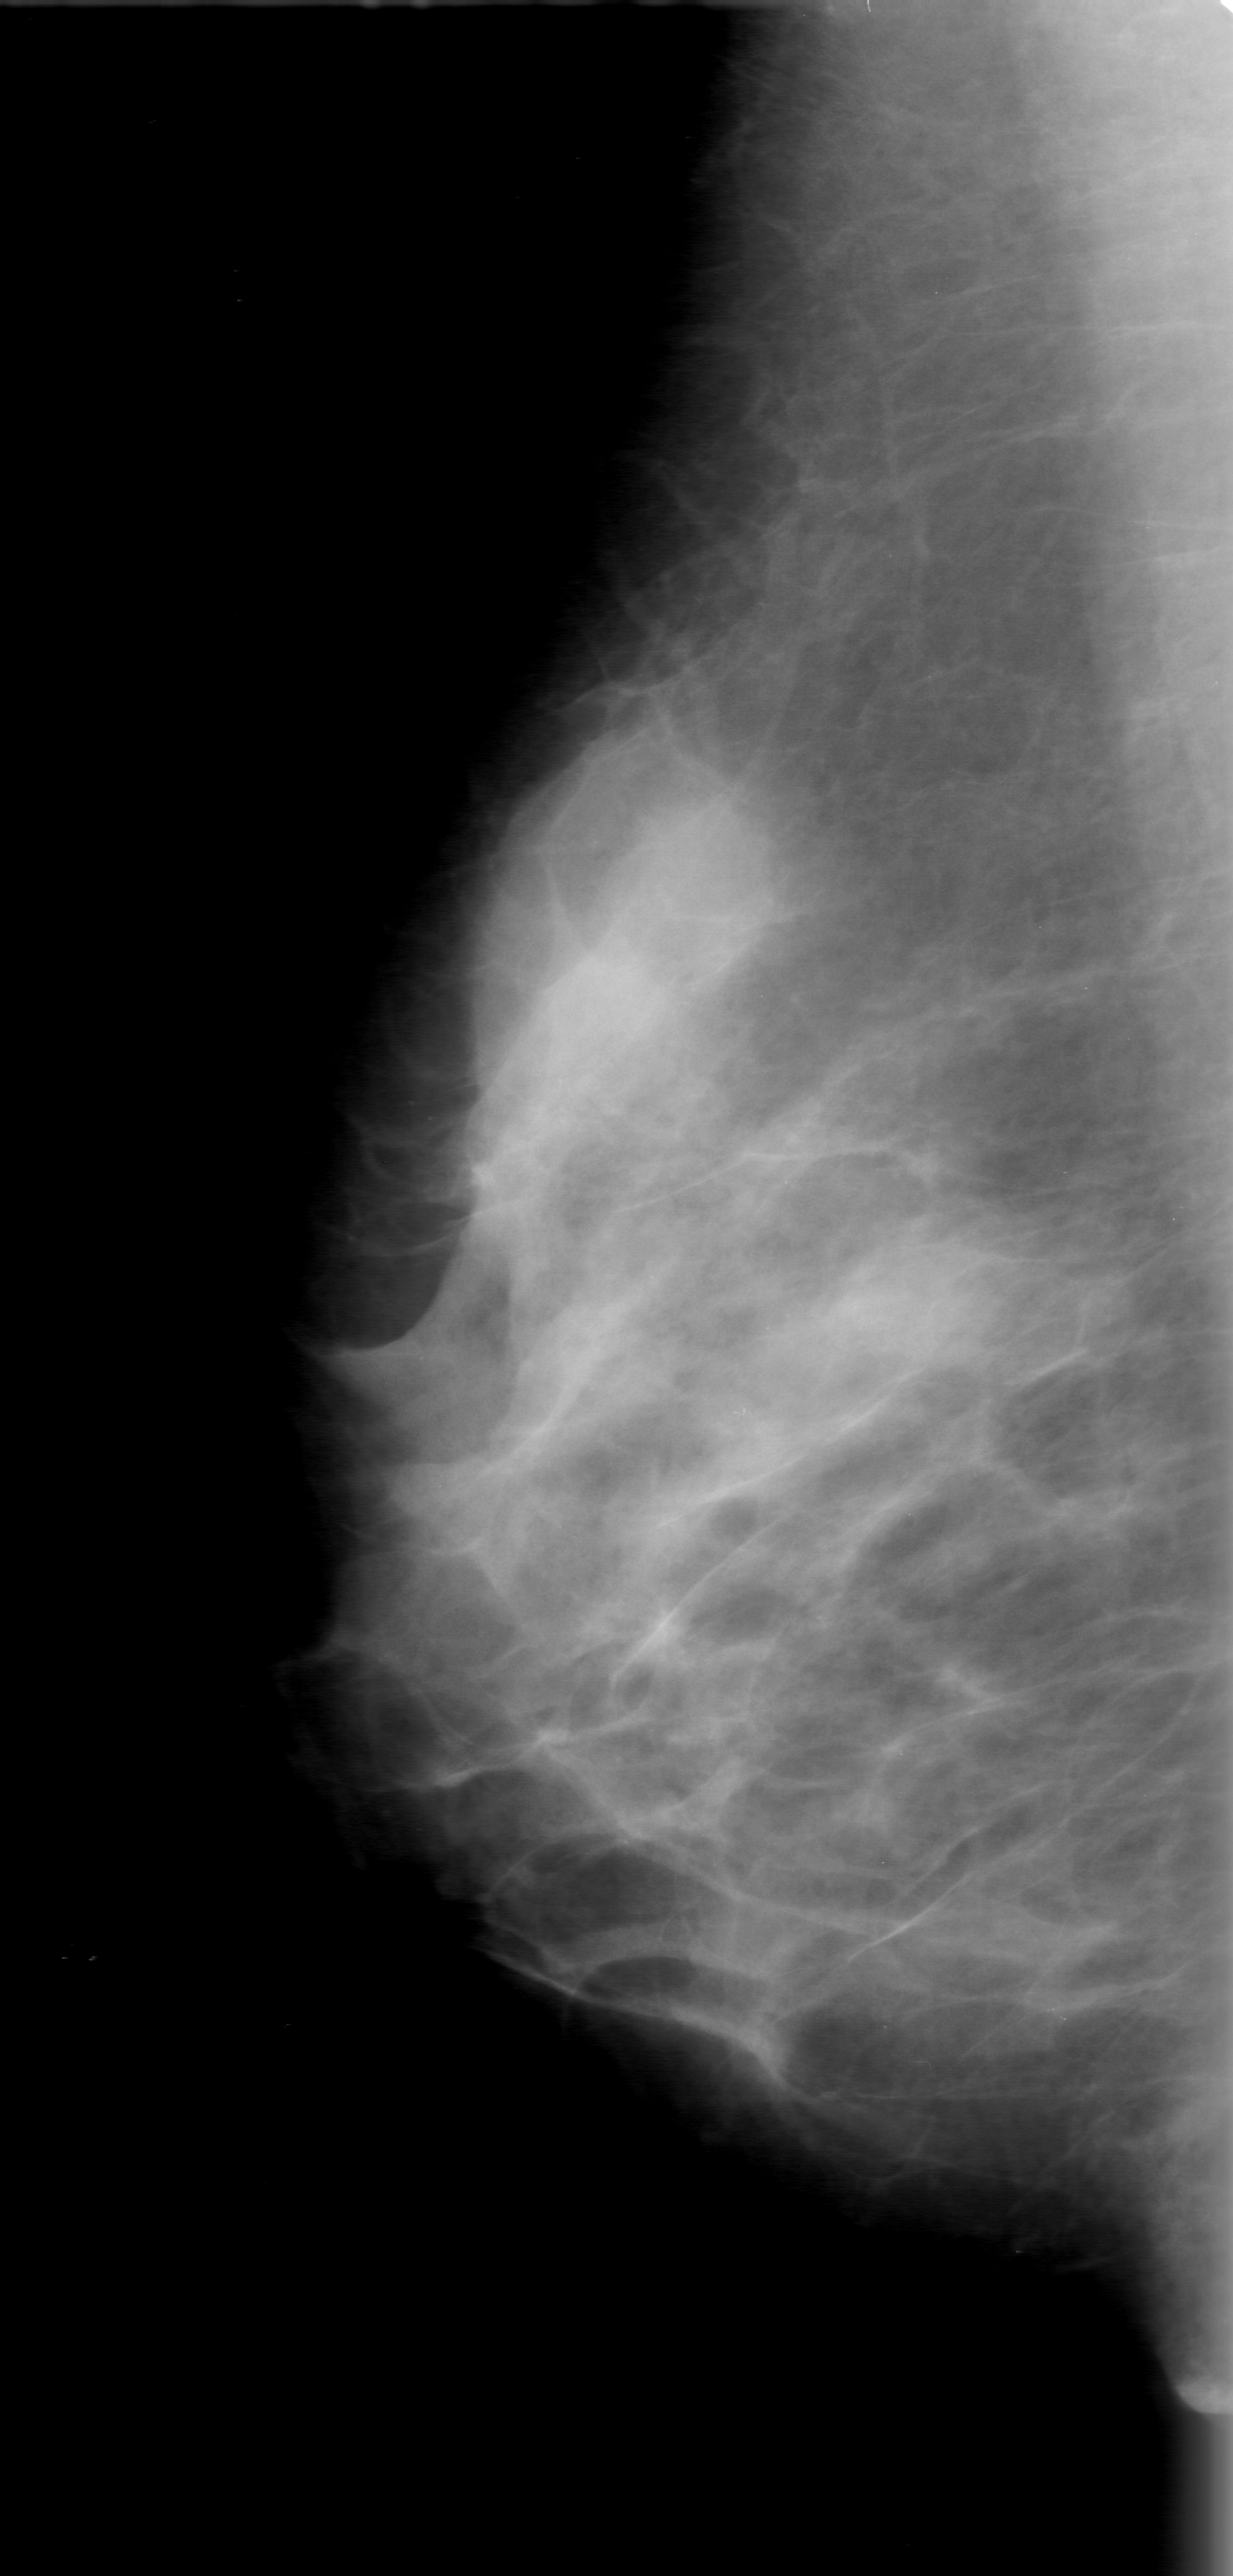
Scanned film-screen mammogram. Right breast. Mediolateral oblique (MLO) view. Breast composition: heterogeneously dense (BI-RADS density category 3 of 4). 1233 × 2576 image matrix.
Expert-marked regions of interest on this image (one box per marked abnormality):
- calcifications, morphology amorphous, distribution segmental; BI-RADS assessment category 0; subtlety rating 3 on a 1 (subtle) to 5 (obvious) scale; pathology (as recorded): benign: box from (x=658, y=1327) to (x=808, y=1488) px